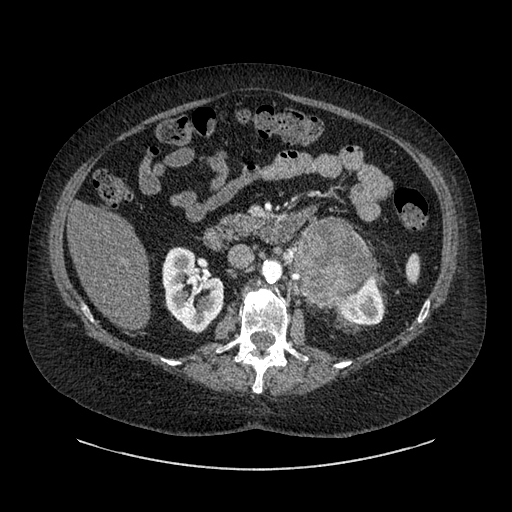
Contrast-enhanced abdominal CT, one axial slice. Slice 520 of 769 in the series (ordered by position). 120 kVp. Intravenous contrast given. Soft-tissue window (W 400 / L 40 HU). 512 × 512 image matrix, field of view 460 × 460 mm. Patient: female, 61 years. From the clinical record (not read from this slice): diagnosis: adrenocortical carcinoma; tumour side: left adrenal; tumour size at pathology: 13 cm; Ki-67 index: 79 %; stage (as recorded): 2.
Outlined on this slice (semi-automatically segmented with operator editing):
- mass: bounding box <293,219,371,303> (left, top, right, bottom; pixels)